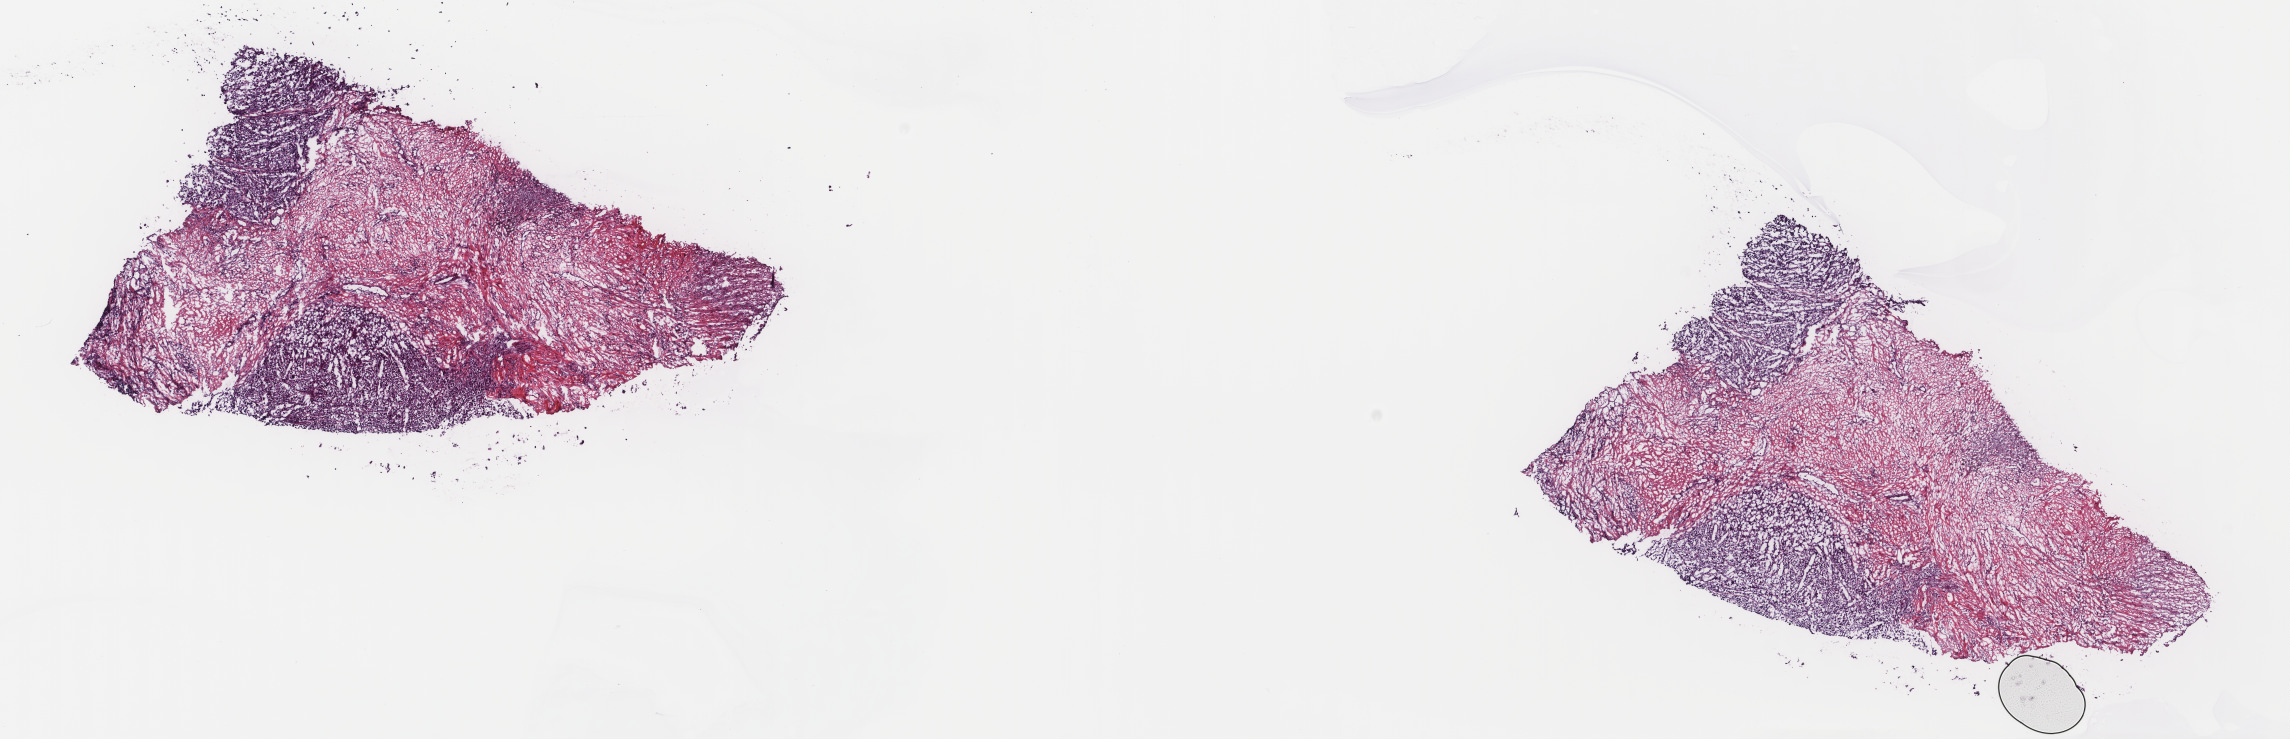
Digitized H&E-stained tissue section (whole slide) — shown as a low-resolution overview of the whole scanned area (about 18.2 x 5.9 mm), frozen section from the top of the tissue portion, metastatic tumour sample, sampled site not recorded. Patient: female, age at initial diagnosis 77 years. Pathologist review of this section (percent, as recorded): tumour cells 35%, tumour nuclei 65%, normal cells 0%, stromal cells 65%, necrosis 0%. Inflammatory infiltration, as recorded: lymphocyte infiltration 0%, monocyte infiltration 0%, neutrophil infiltration 0%.
• this section: metastatic tumour tissue
• patient diagnosis: Malignant melanoma, NOS